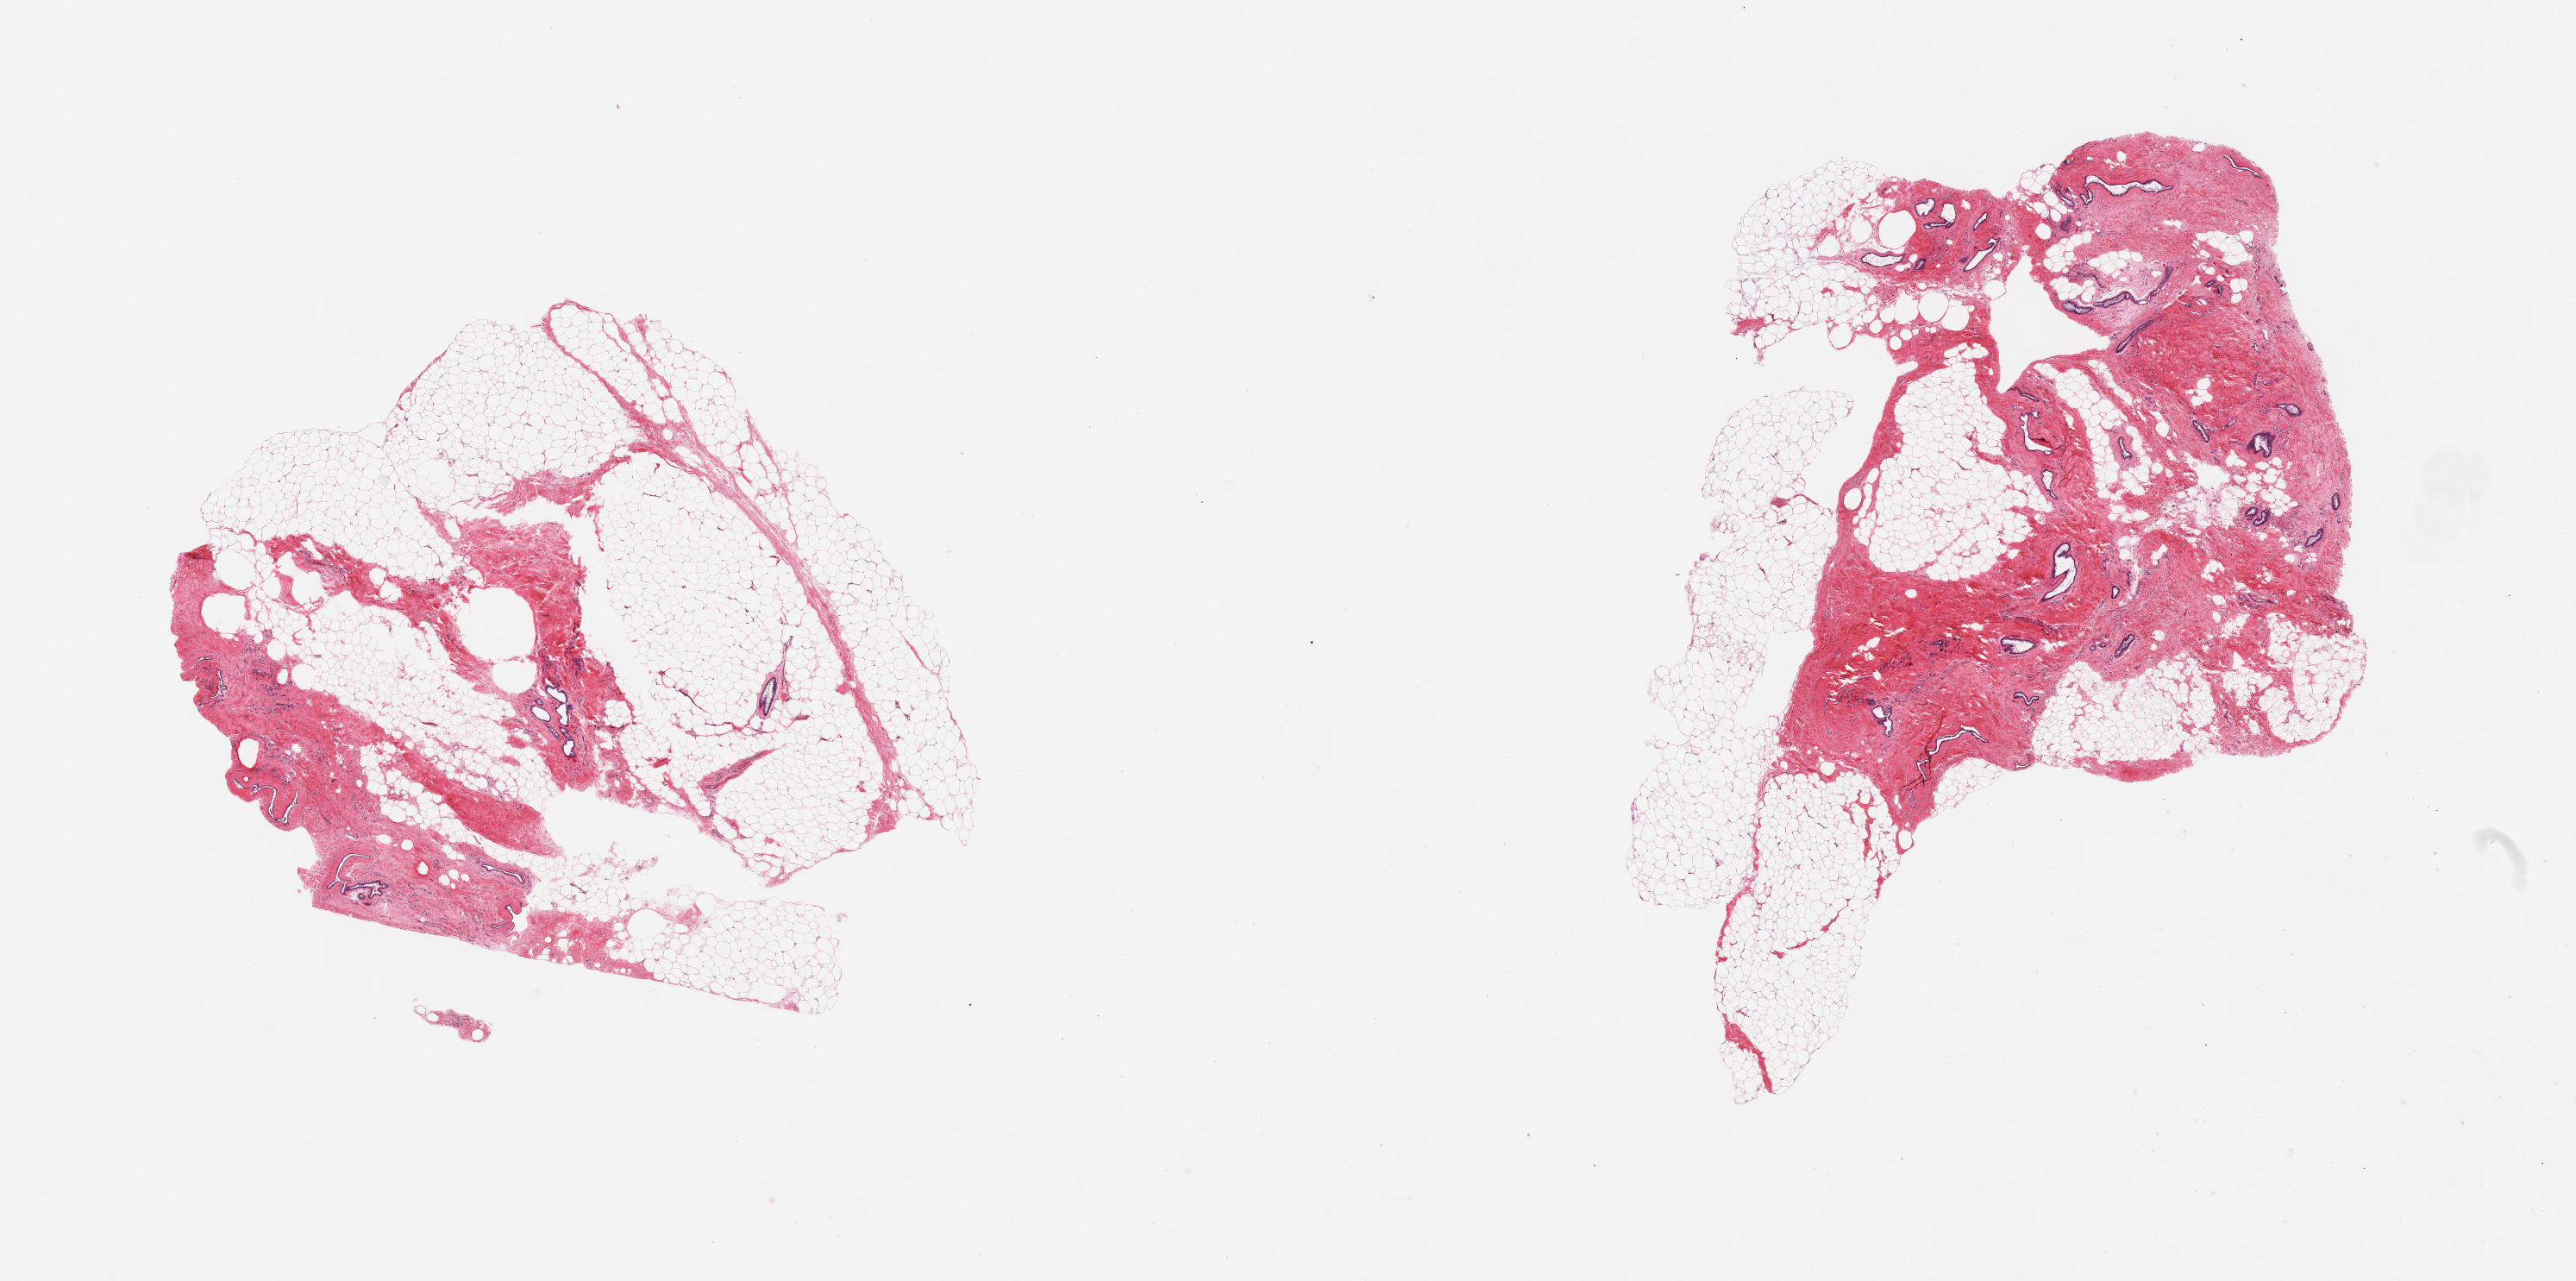
Hematoxylin and eosin (H&E) whole-slide image — whole scanned area (about 23.6 x 11.7 mm, slide scanned at 20x) shown as a low-resolution overview. PAXgene-fixed paraffin-embedded (PFPE) section. Section of breast (target tissue). Donor tissue sample. Male donor.
Reviewer comment on this tissue sample: 2 pieces; fibrofatty tissue with ducts.